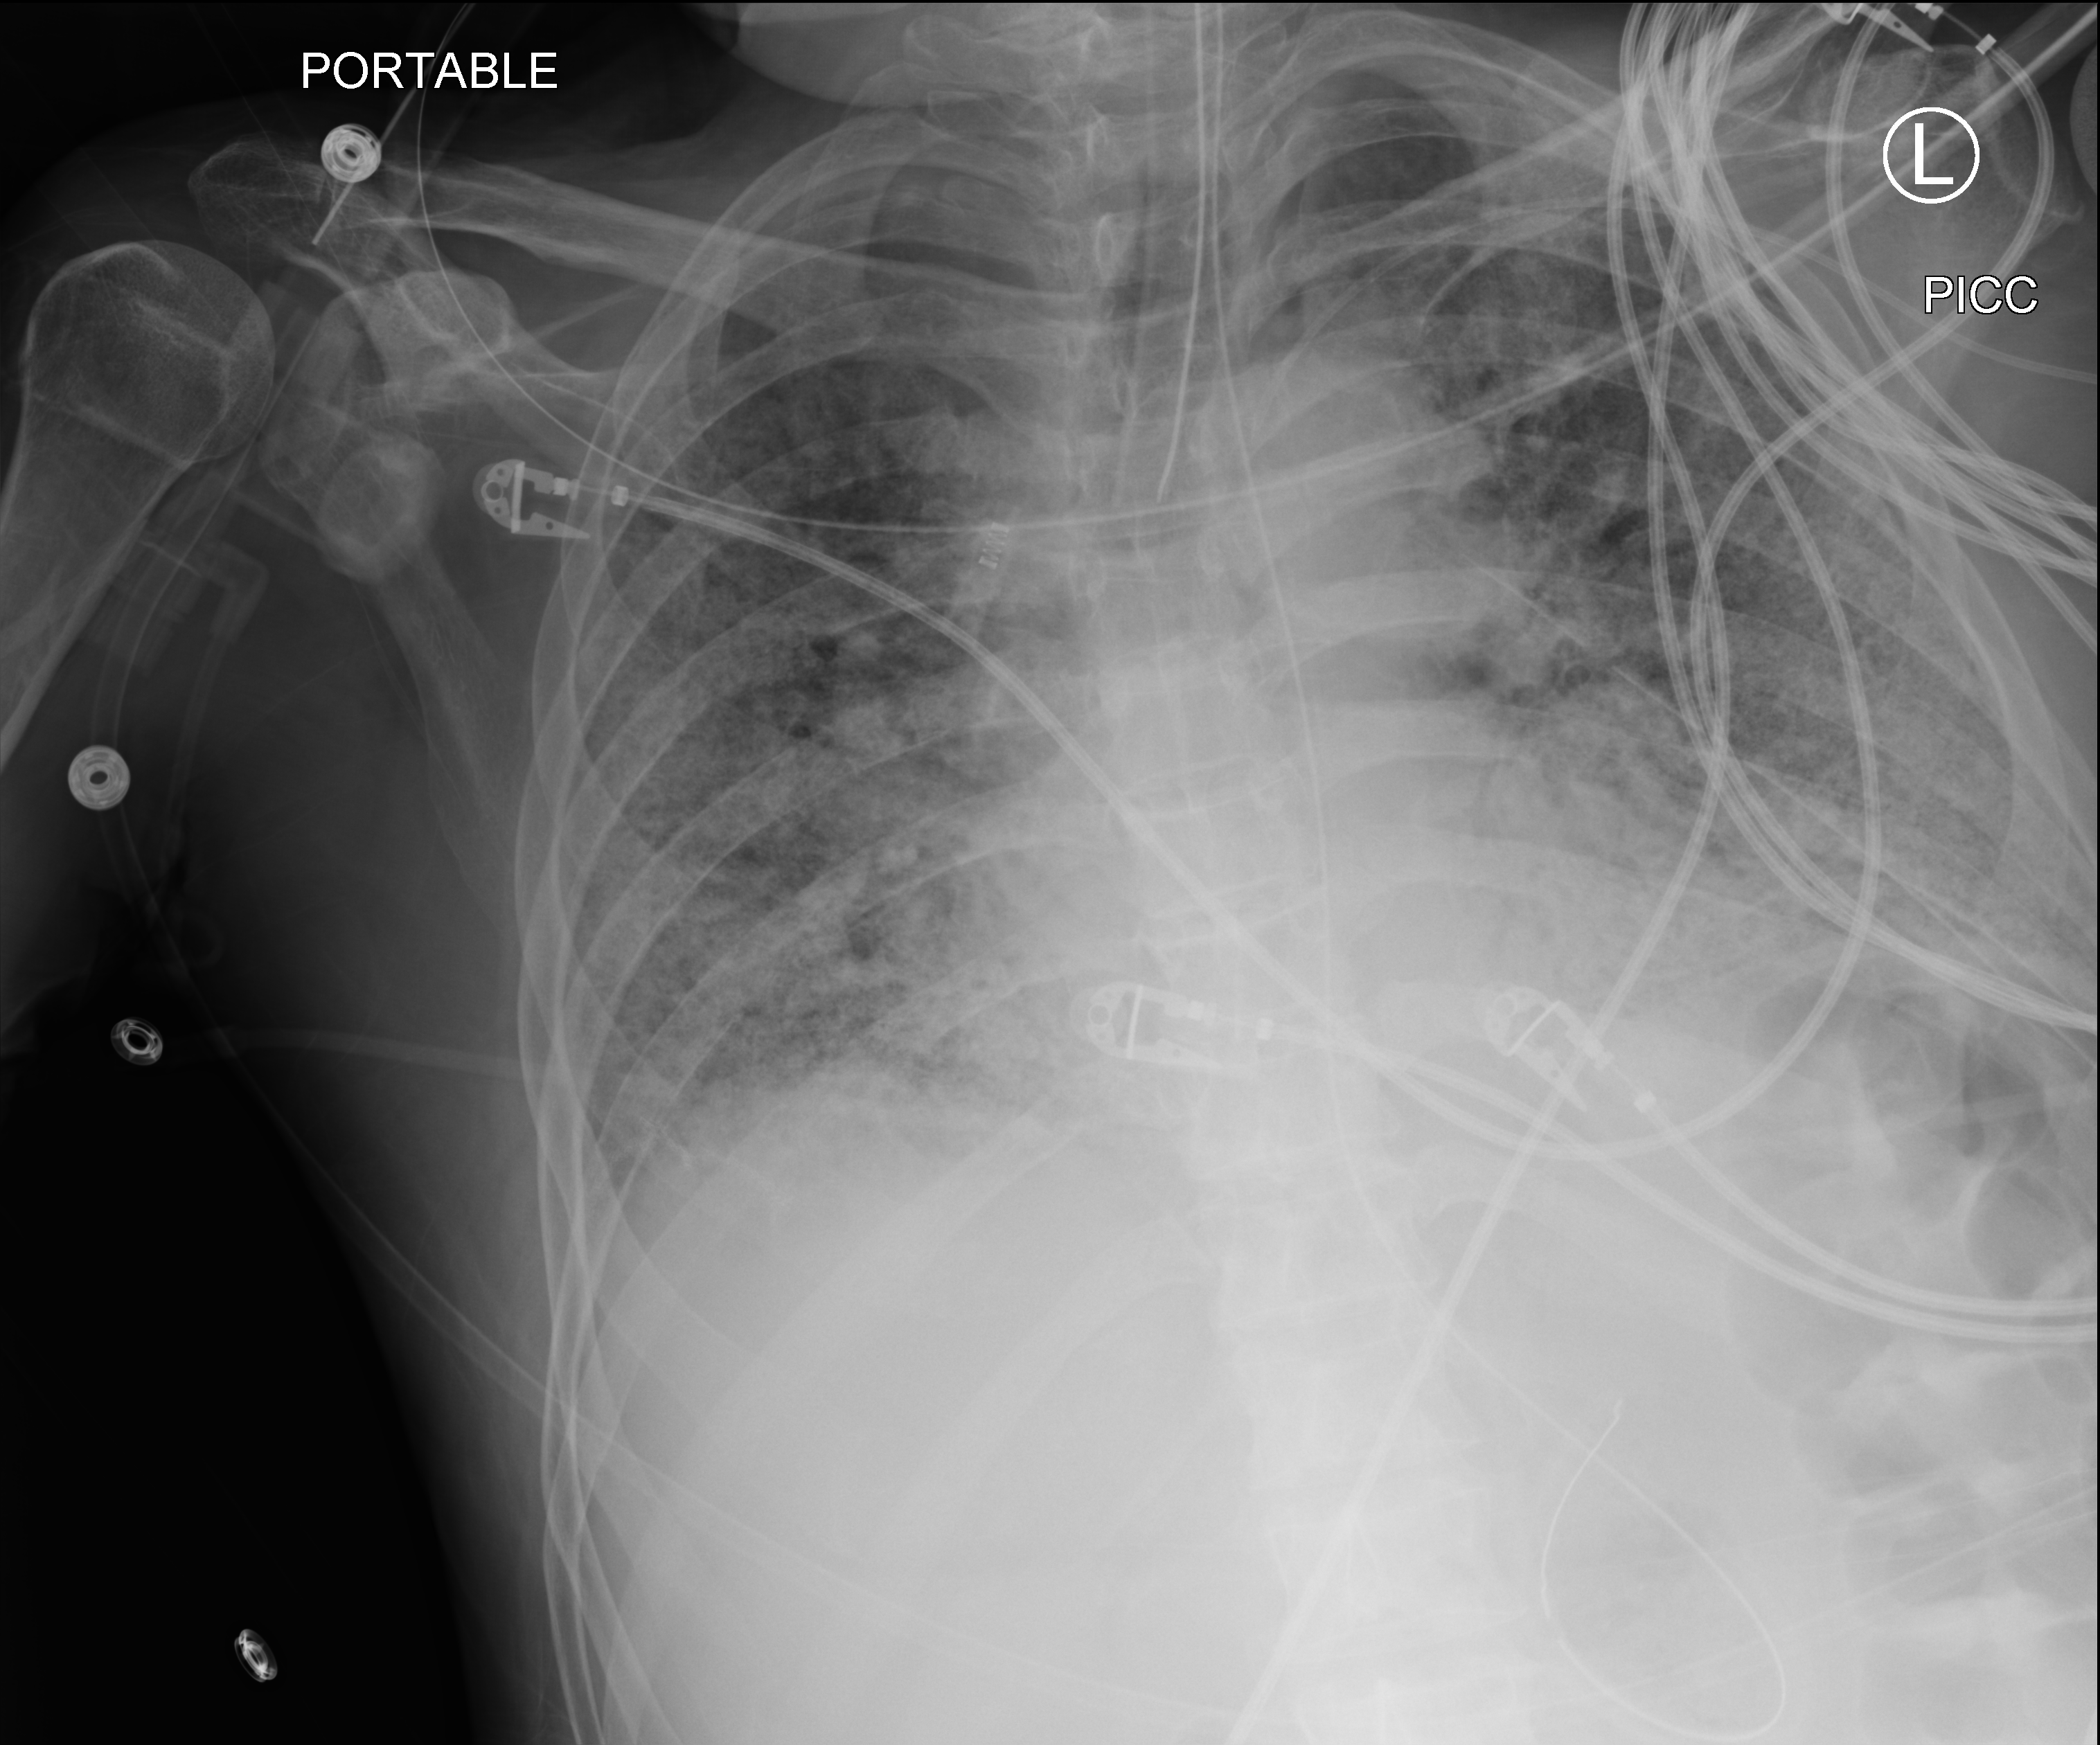
Portable chest radiograph; anteroposterior (AP) projection. Male patient hospitalised with COVID-19, age 60–74 years.
Admission-level facts for this patient (not findings on this image; timing relative to this image not recorded):
- length of hospital stay: 54 days
- admitted to intensive care during this hospital stay: yes
- mechanically ventilated during this hospital stay: yes